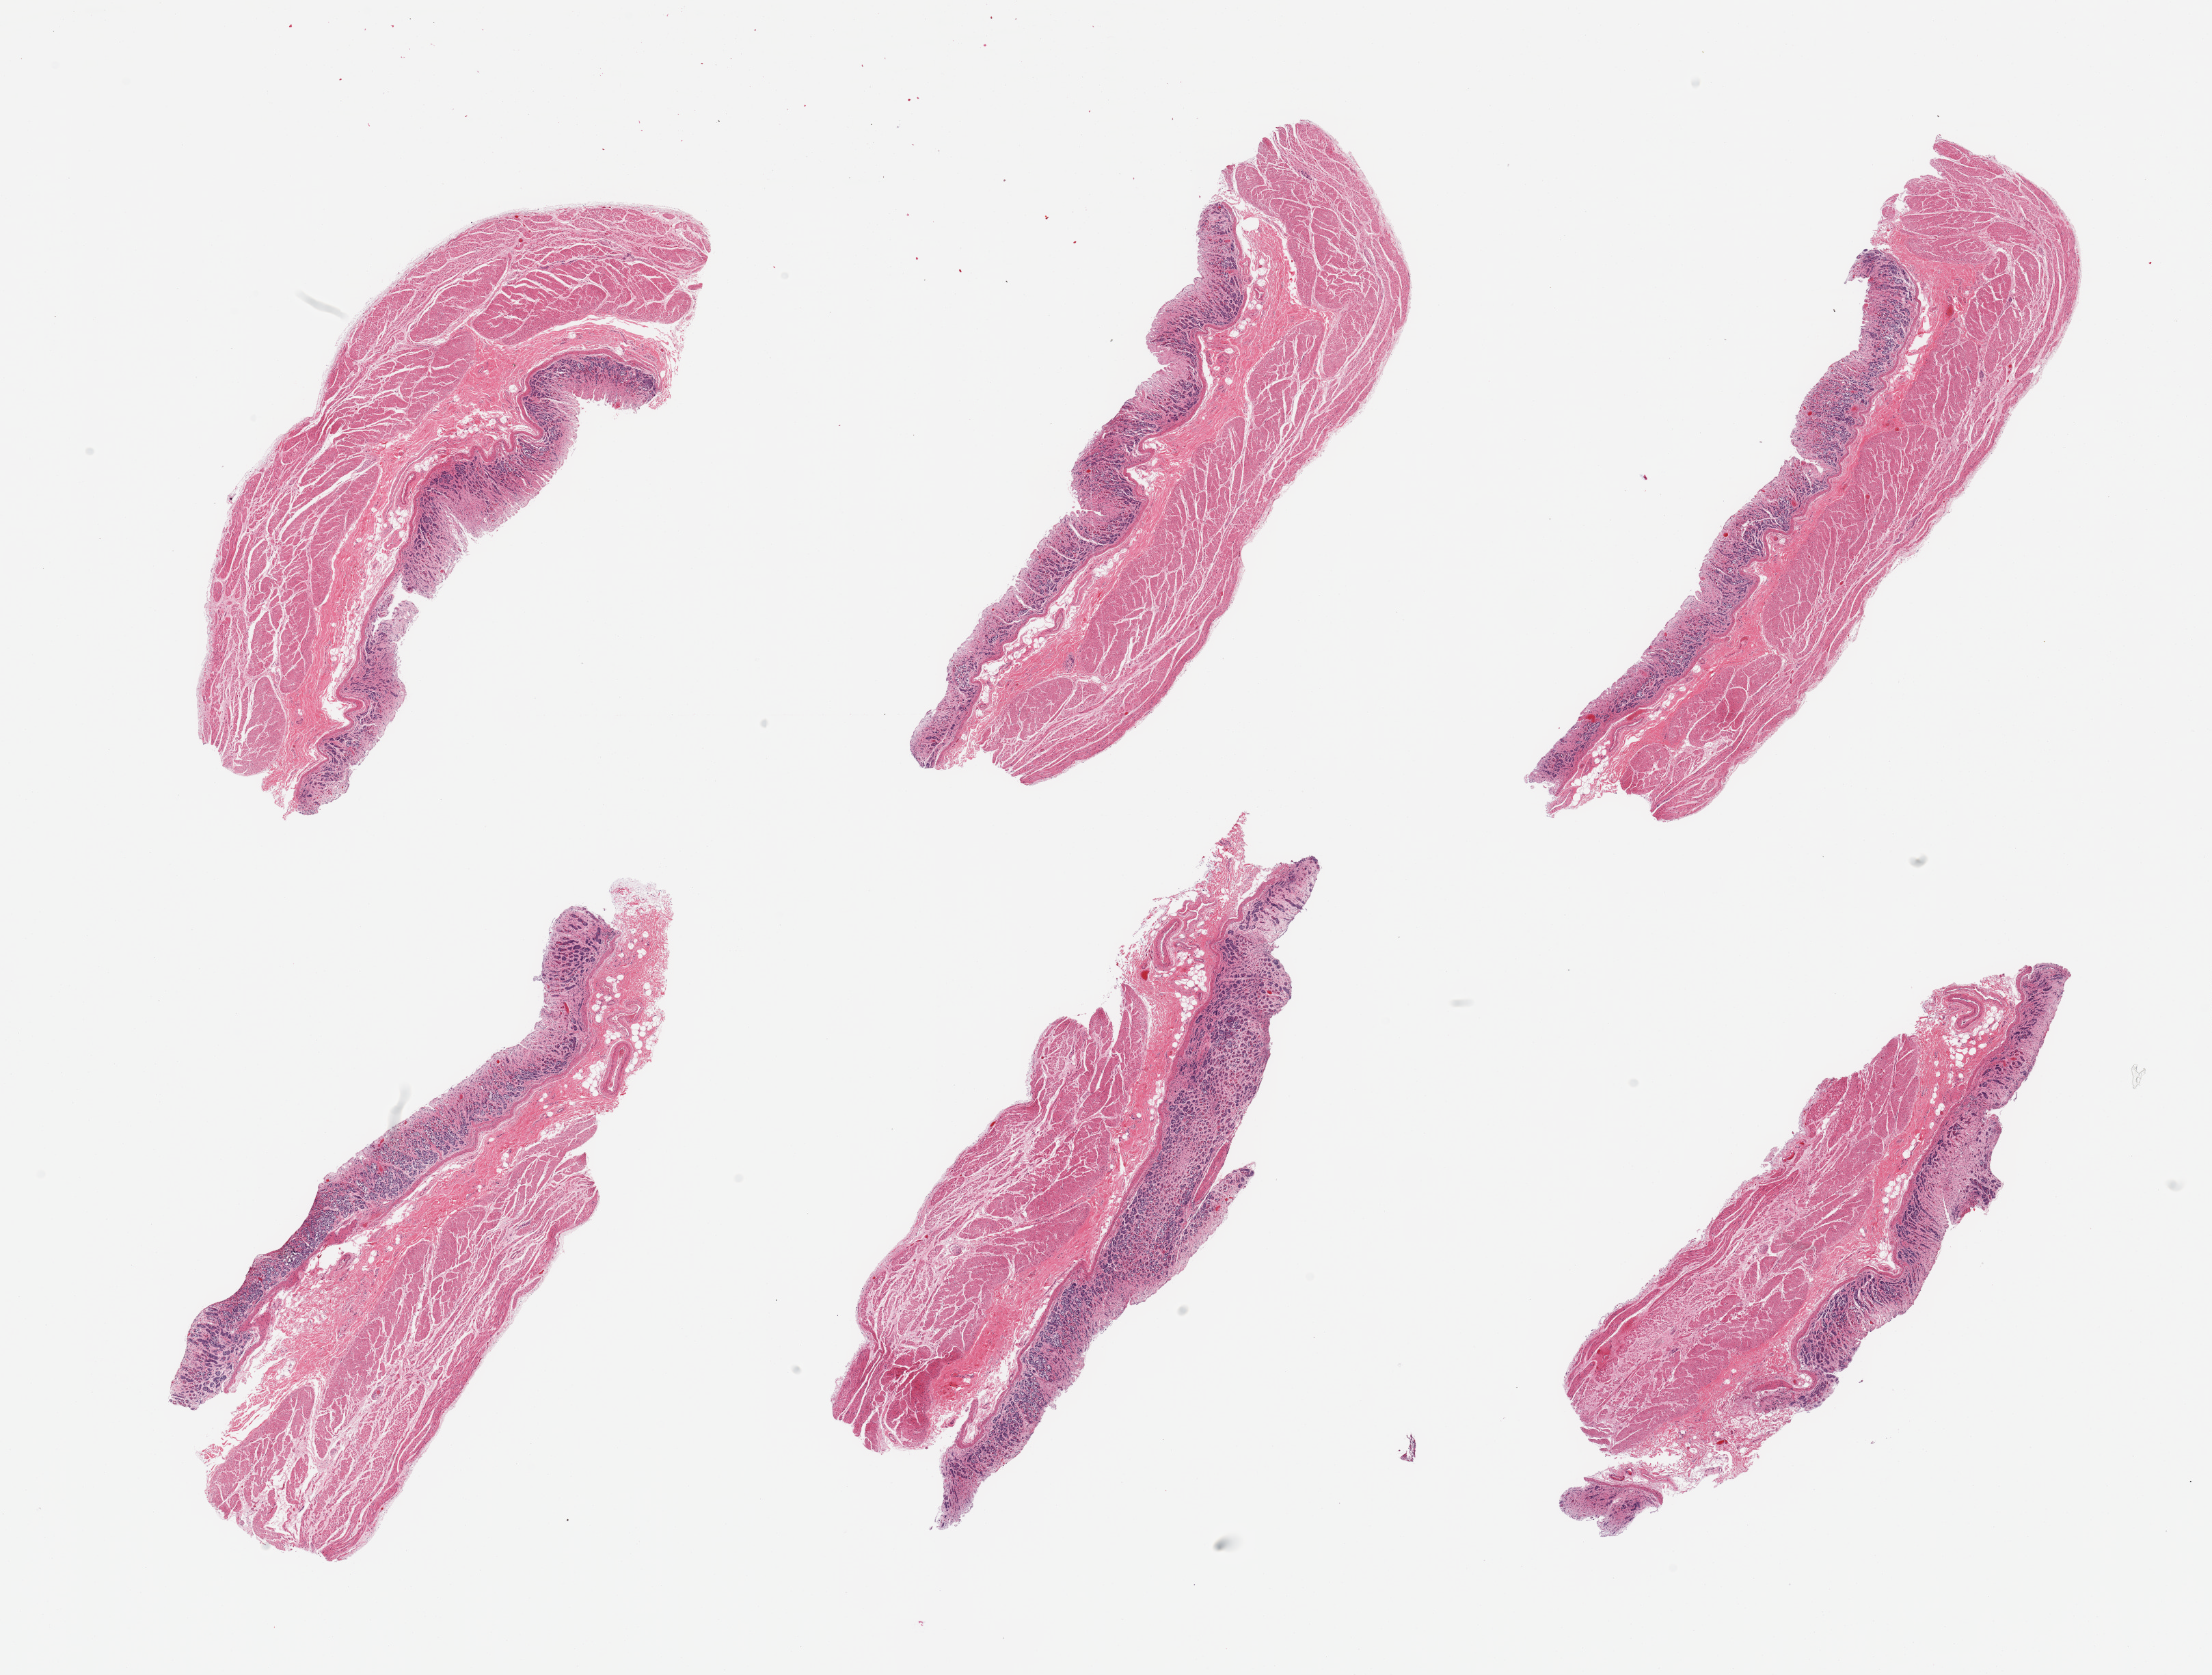
Whole-slide image, H&E stain — whole scanned area (about 25.6 x 19.4 mm) shown as a low-resolution overview, PAXgene-fixed, paraffin-embedded tissue, section of stomach (target tissue), donor tissue sample.
- review note (as recorded): 6 pieces; glands largely autolyzed